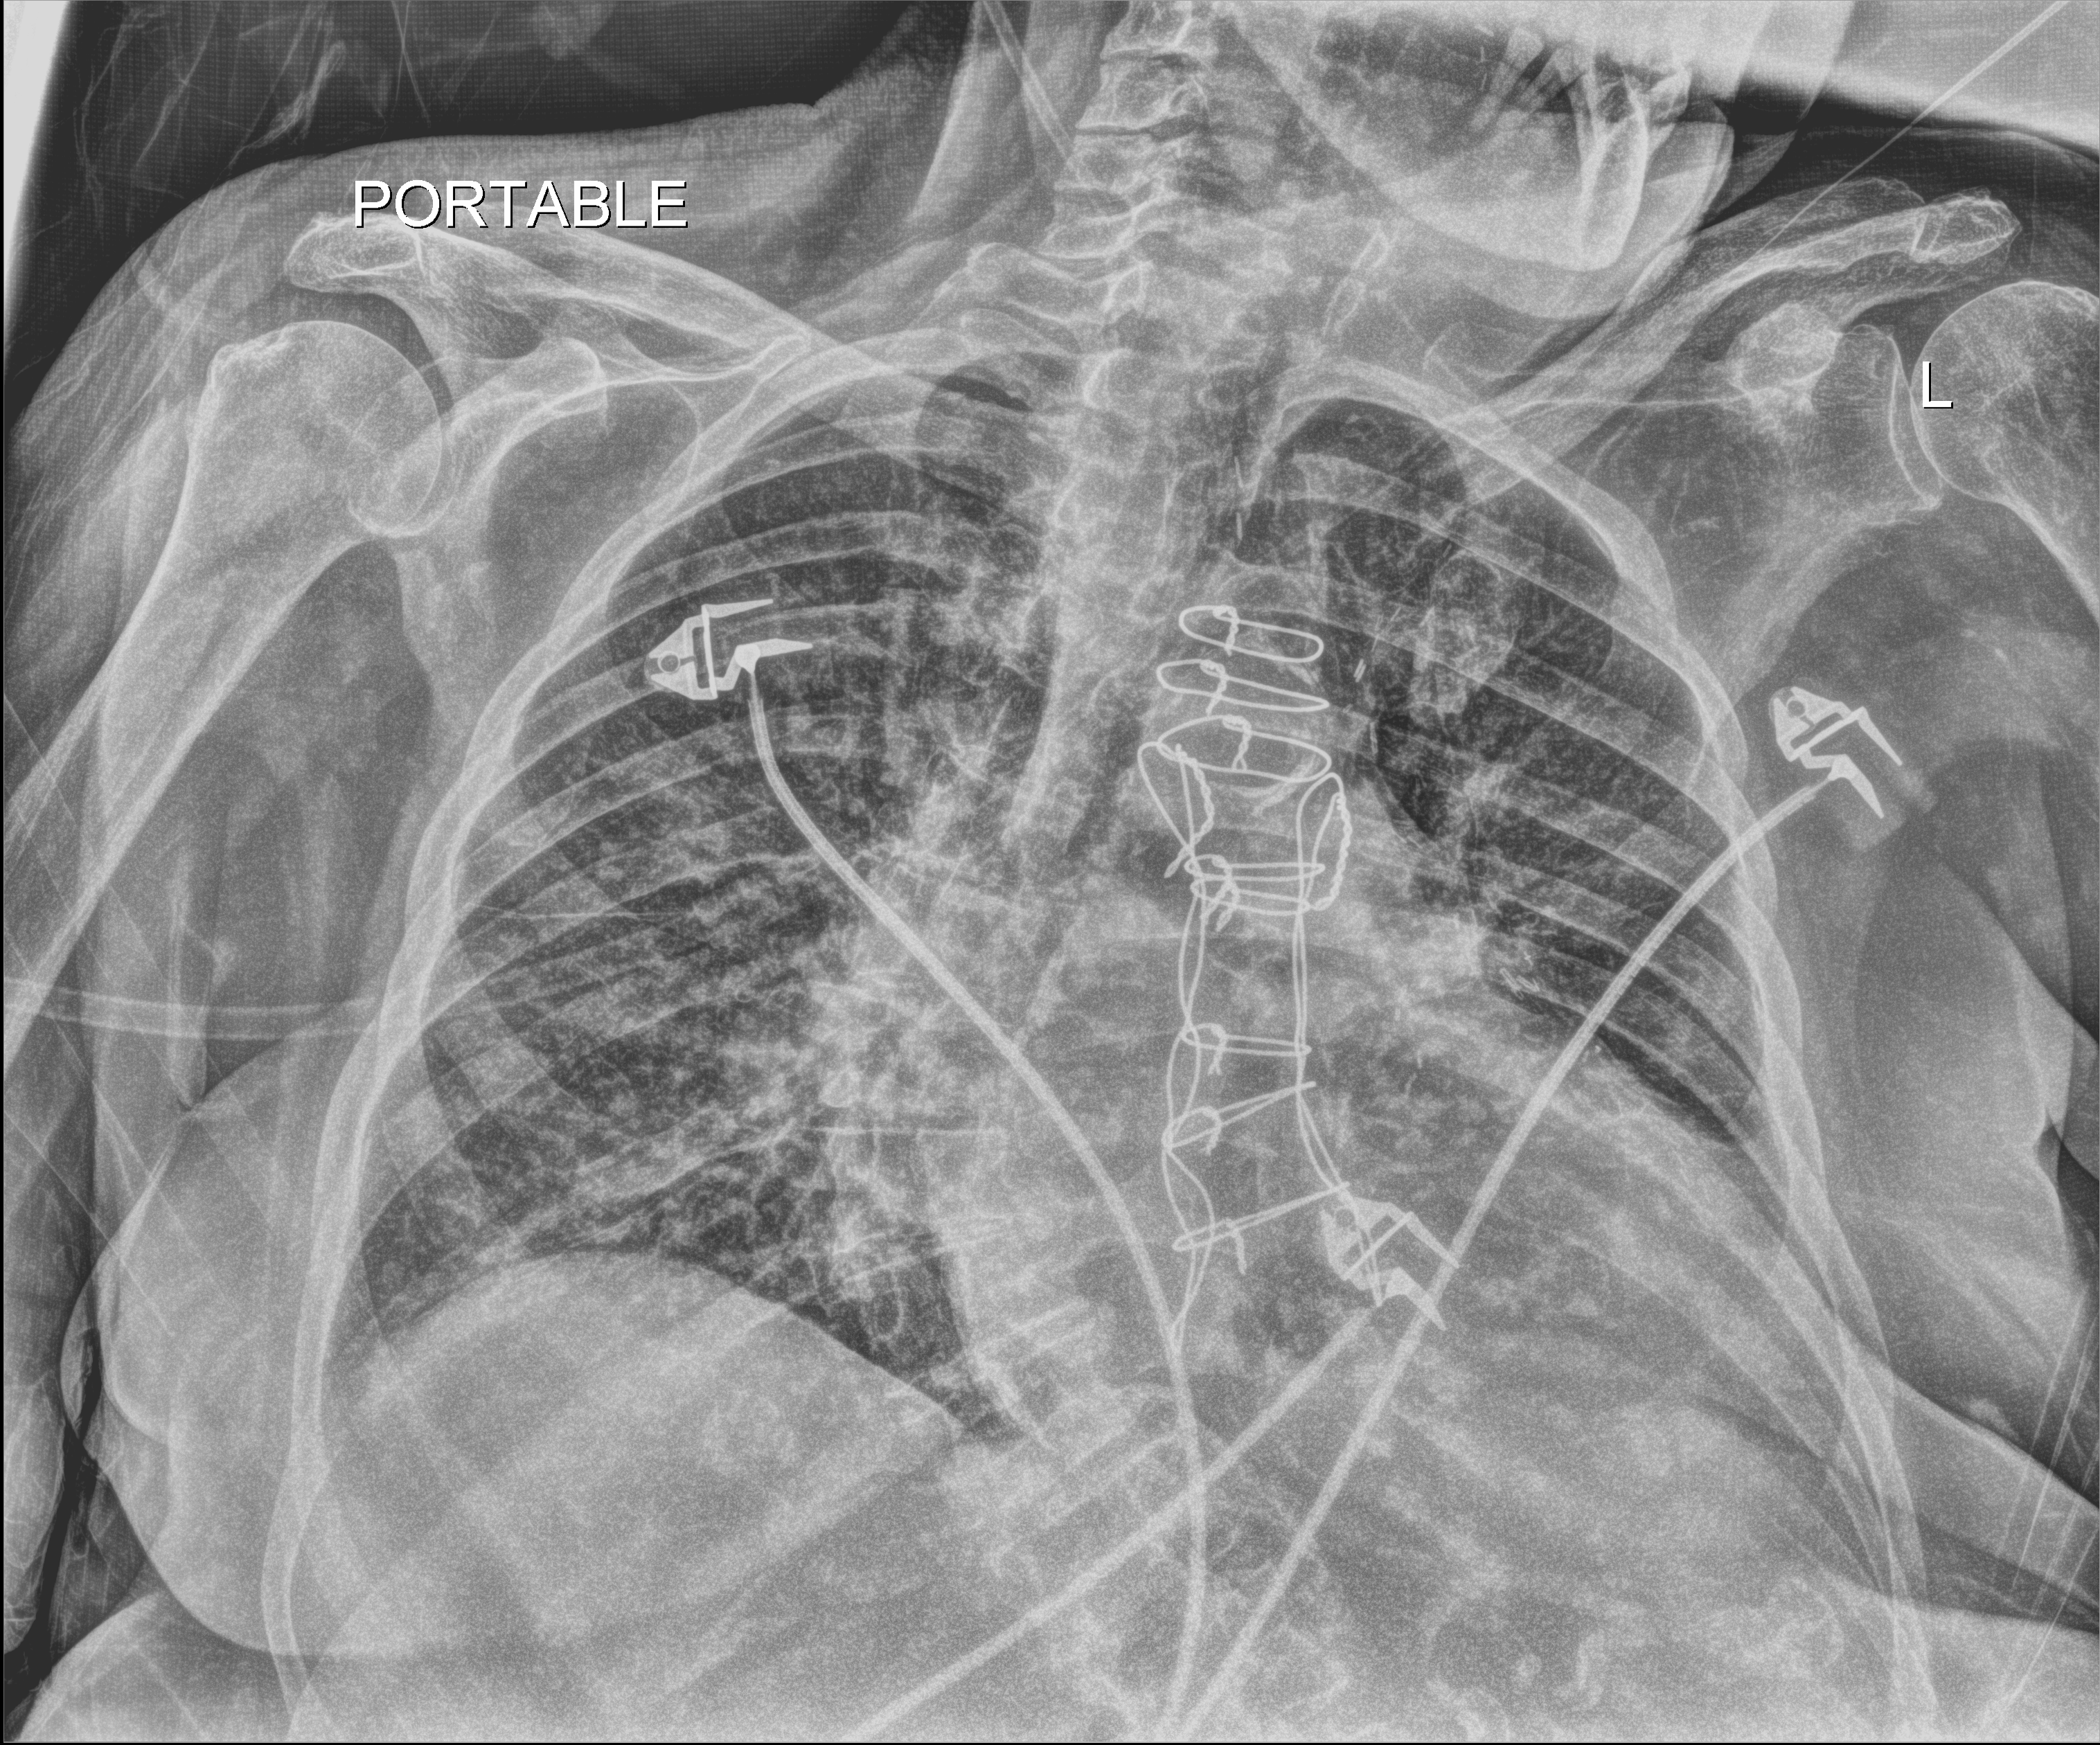
Chest X-ray. Patient hospitalised with COVID-19; female, aged 75–90 years.
From the hospital-stay record, not from the radiograph (when in the stay this image was taken is not recorded):
- admitted to intensive care during this hospital stay: no